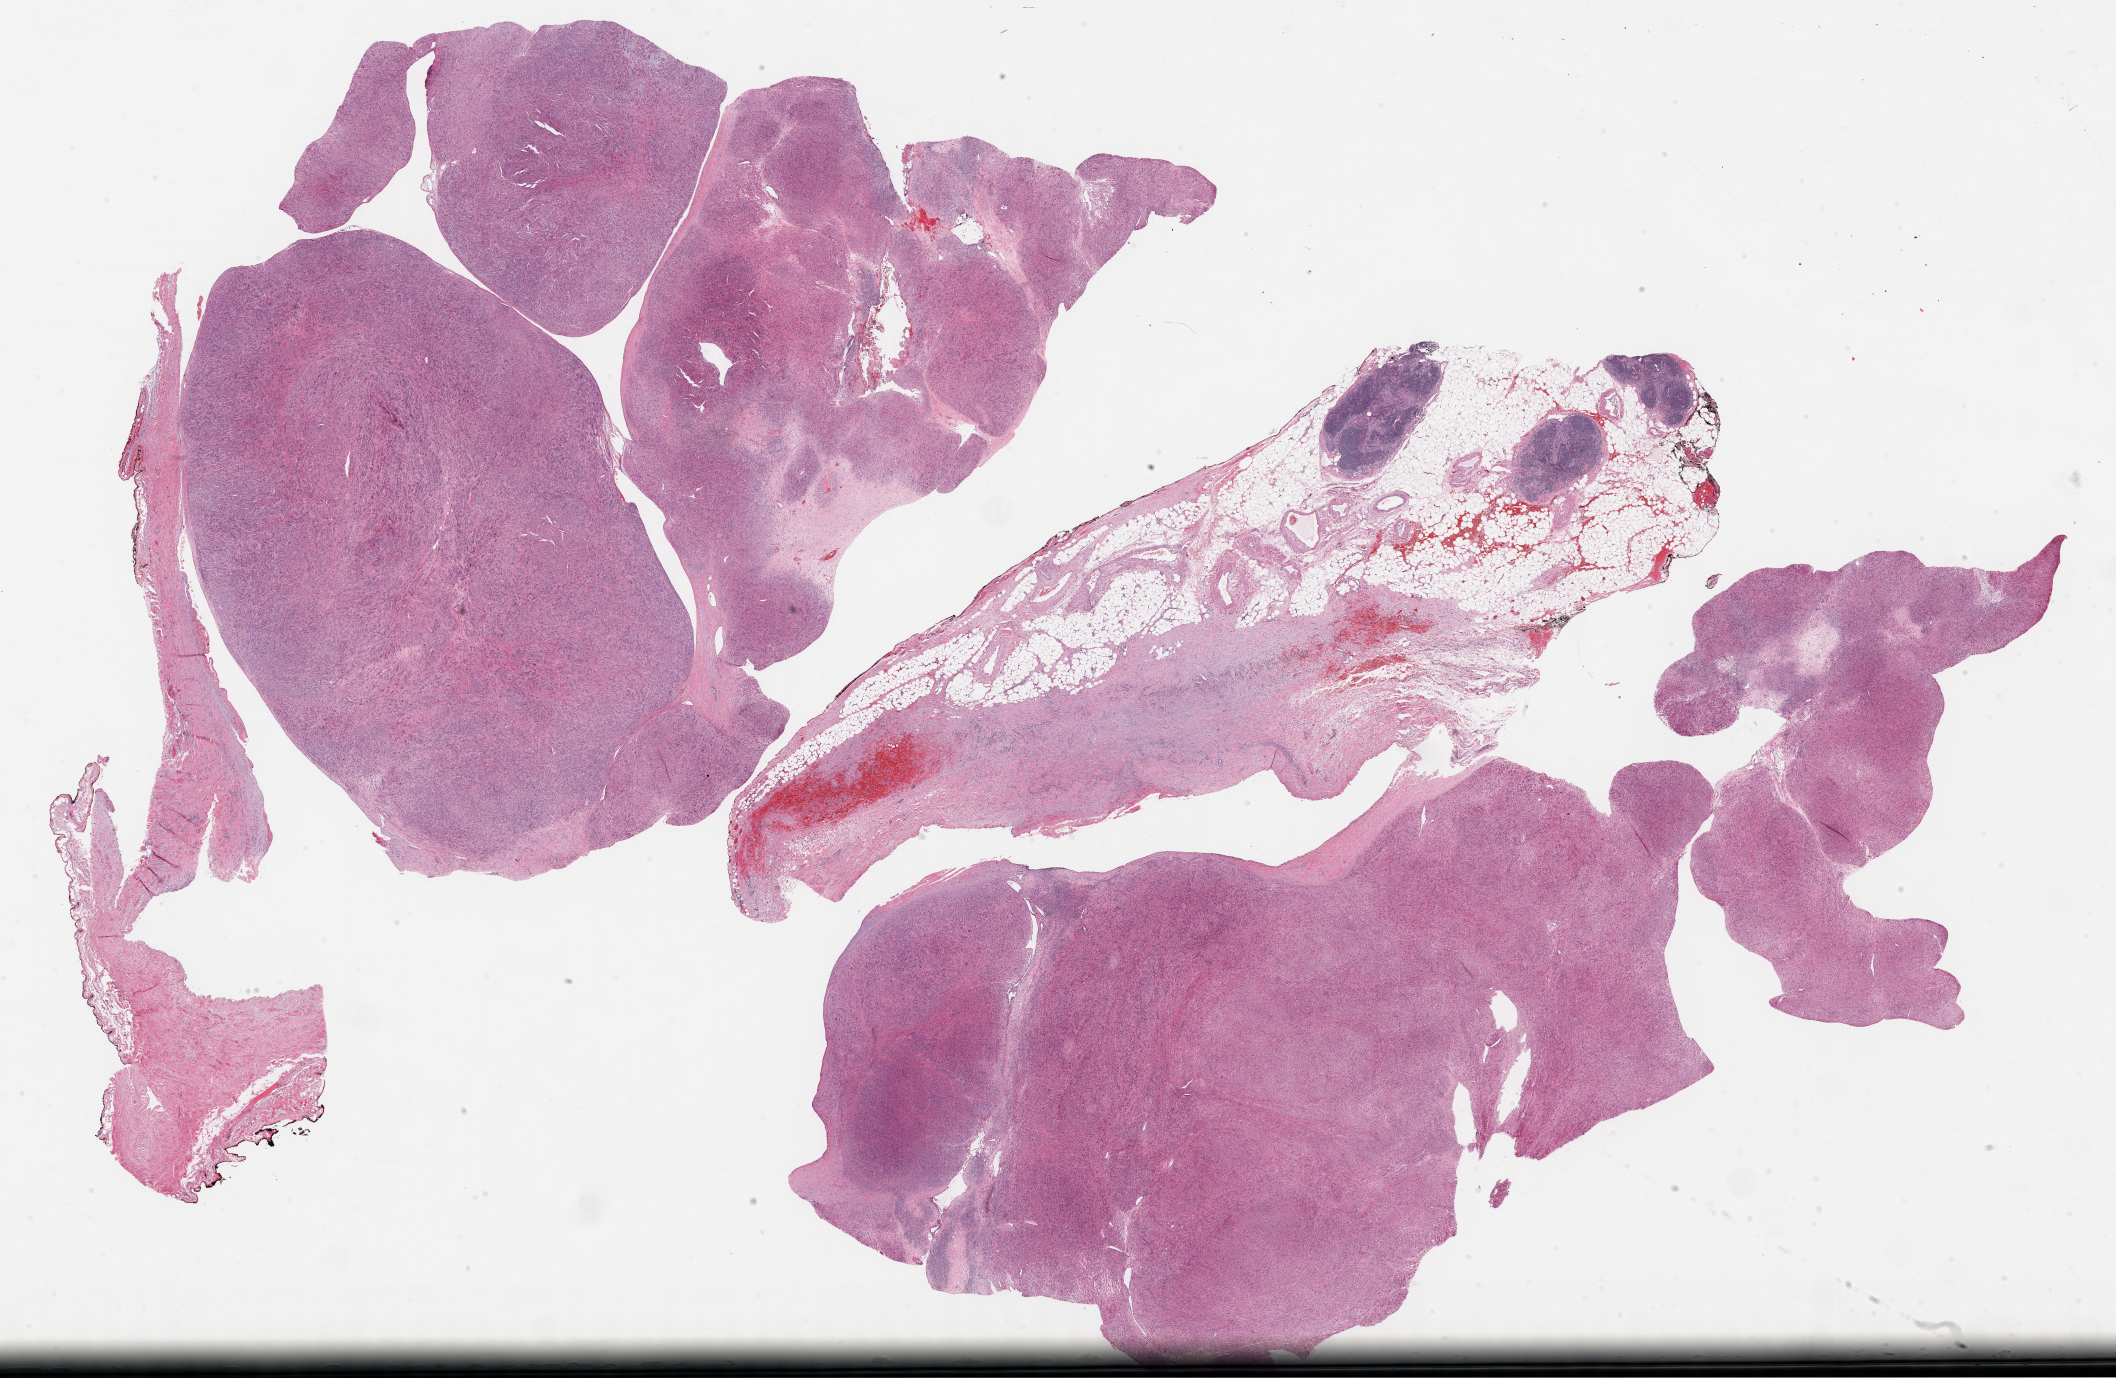
Digitized H&E-stained tissue section (whole slide) — whole scanned area (about 34.2 x 22.3 mm) shown as a low-resolution overview; formalin-fixed paraffin-embedded (FFPE) diagnostic section; retroperitoneum and peritoneum, primary tumour sample. Female, age 56 years at initial diagnosis.
• histologic diagnosis: Leiomyosarcoma, NOS (retroperitoneum)